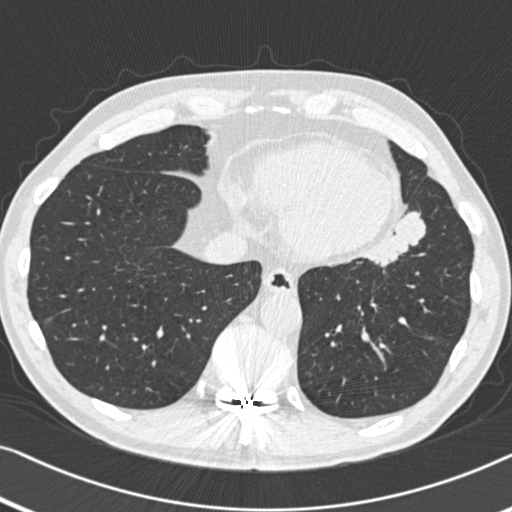
Low-dose screening chest CT, one axial slice; position 131 of 383 along the scan axis; reconstruction kernel B30f; 120 kVp; lung window (W 1500 / L -600 HU); 1 mm slice thickness; 512 × 512 image matrix, field of view 332 × 332 mm.
Outlined on this slice (expert manual segmentation):
- lesion 1 (tumor, upper lobe of left lung): bounding box (x1, y1, x2, y2) in pixels: (375, 211, 426, 267)